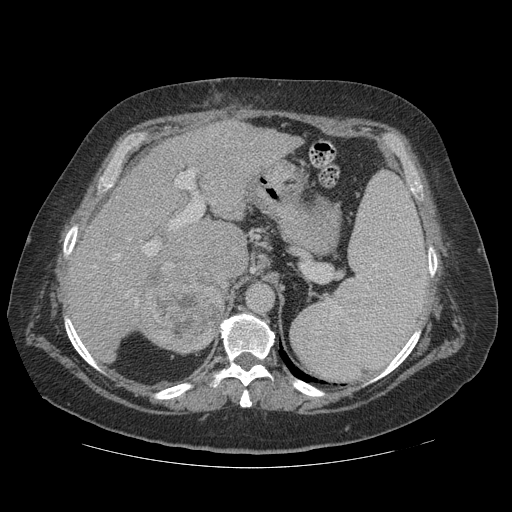
Contrast-enhanced abdominal CT (liver protocol), one axial slice. Slice 80 of 121 in the series (ordered by position). Soft-tissue window (W 400 / L 40 HU). 2.5 mm slice thickness. 512 × 512 image matrix, field of view 420 × 420 mm. From the clinical record (not read from this slice): diagnosis: hepatocellular carcinoma (patient treated with transarterial chemoembolisation; whether this scan precedes or follows treatment is not stated here); TNM stage (as recorded): Stage-IIIA.
Outlined on this slice (semi-automatic segmentation, software-assisted and operator-edited):
- liver parenchyma outside the tumour (the mass and vessels are separate outlines, so this box may not span the whole liver): bounding box [x1, y1, x2, y2] px = [64, 120, 302, 360]
- mass: [134, 247, 229, 353]
- liver vessels: [89, 134, 275, 312]